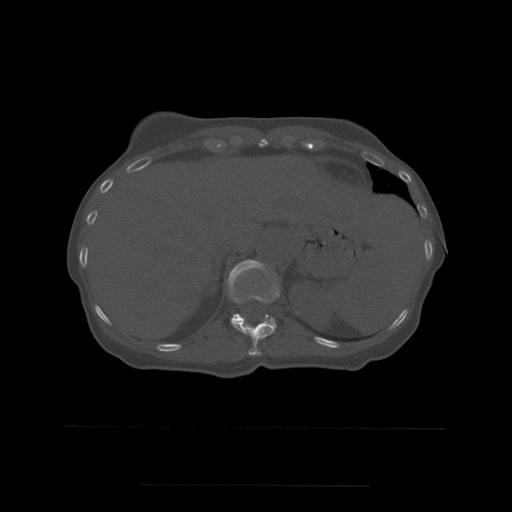
CT including the spine, one axial slice; slice 272 of 544 in the series (ordered by position); bone window (W 1800 / L 400 HU); 512 × 512 image matrix, field of view 350 × 350 mm. Patient age 58 years. From the clinical record (not read from this slice): primary cancer: lung.
Annotated regions visible in this slice (semi-automatic segmentation, software-assisted and operator-edited):
- T11 vertebra: box from (x=231, y=281) to (x=280, y=356) px
- T12 vertebra: (x=228, y=260)–(x=277, y=329)